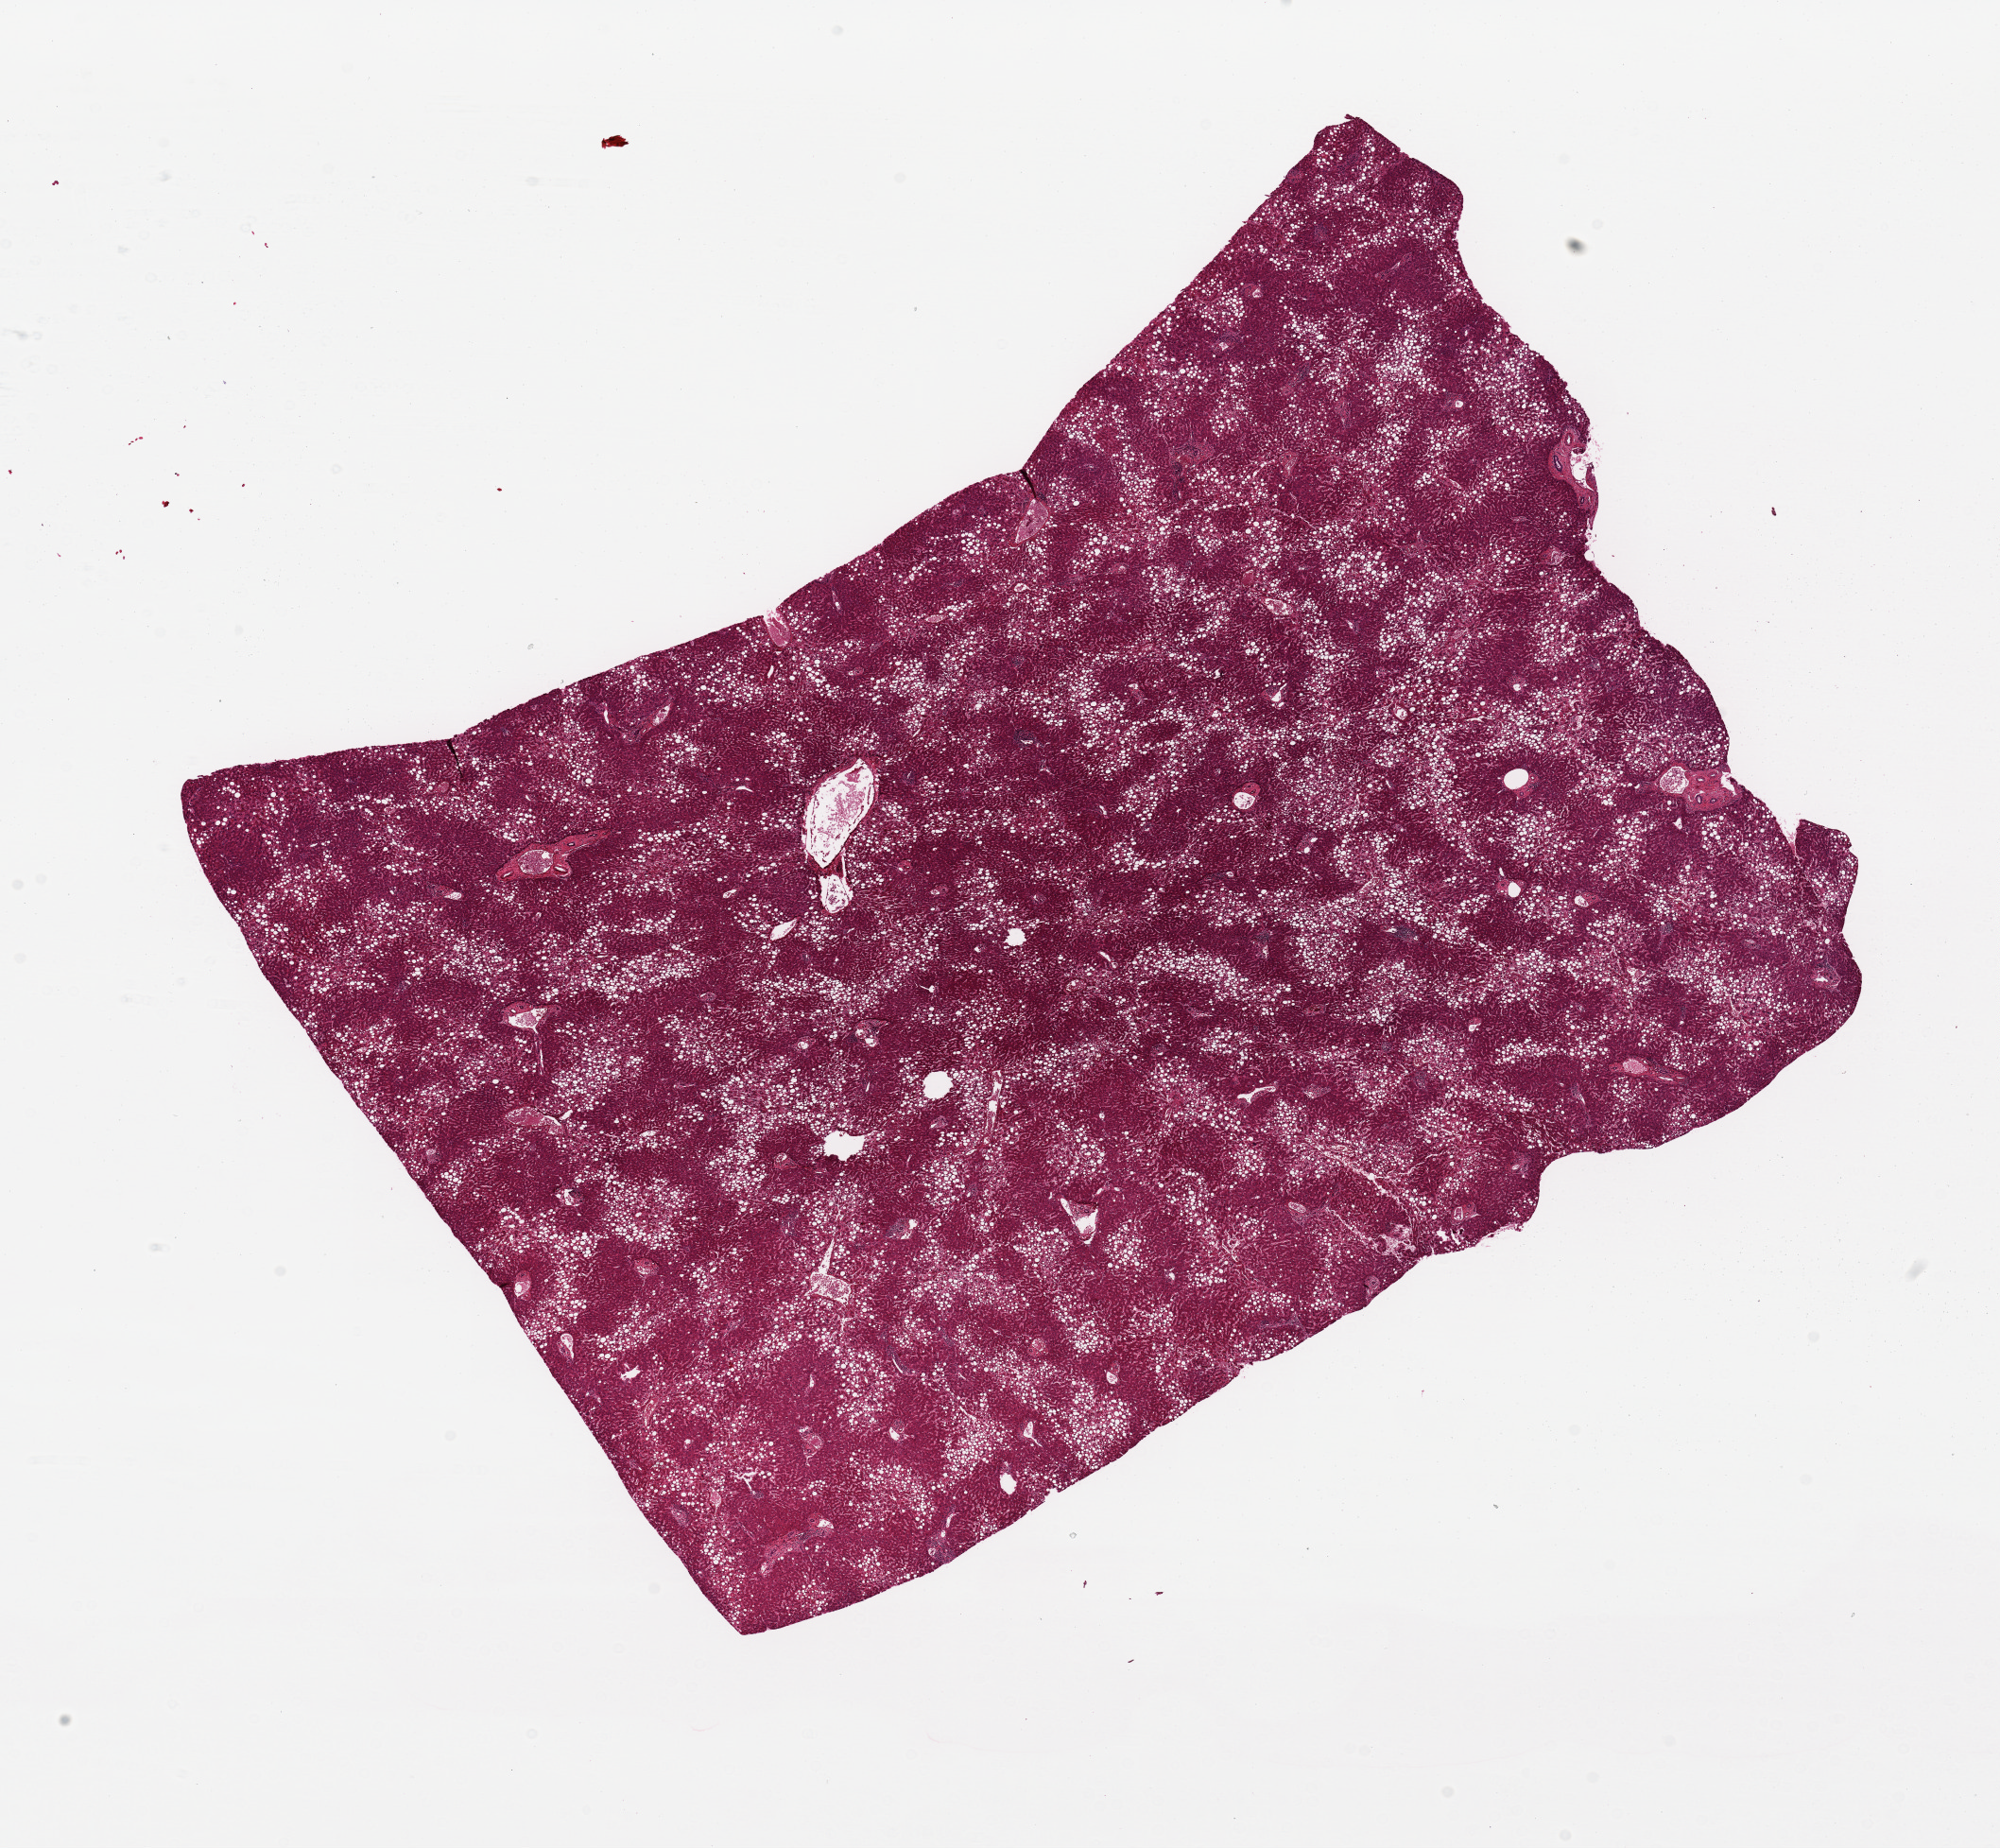
Haematoxylin and eosin whole-slide image, whole scanned area (about 16.7 x 15.5 mm, slide scanned at 20x) shown as a low-resolution overview; PAXgene-fixed, paraffin-embedded tissue; sampled site (target tissue): liver; tissue donor sample. Donor sex: male.
• reviewer comment on this tissue sample: 50-60% macrovesicular steatosis